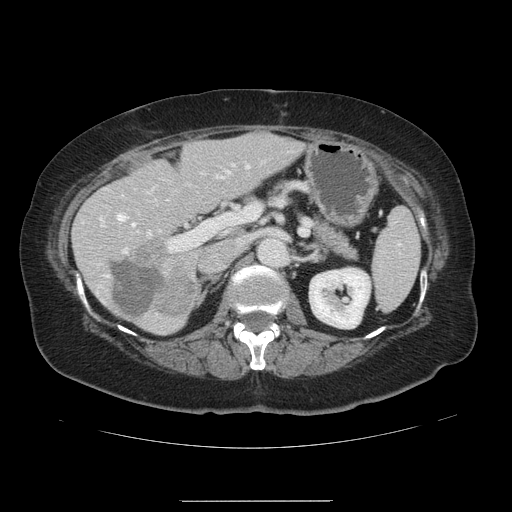
Contrast-enhanced abdominal CT, one axial slice; intravenous contrast given; soft-tissue window (W 400 / L 40 HU); 2.5 mm slice thickness; 512 × 512 image matrix. Female patient, age 74 years. From the clinical record (not read from this slice): diagnosis: colorectal cancer liver metastases, imaged before liver resection; multiple liver metastases: yes; largest metastasis: 7 cm; disease in both lobes: yes.
Annotated regions visible in this slice (manually delineated by an expert):
- hepatic veins: bounding box <117,188,157,228> (left, top, right, bottom; pixels)
- liver: <74,133,301,333>
- planned liver remnant (the part of the liver to remain after resection): <78,133,301,333>
- portal vein (with intrahepatic branches): <99,164,248,253>
- liver metastasis: <111,262,165,317>
- liver metastasis: <134,242,195,316>